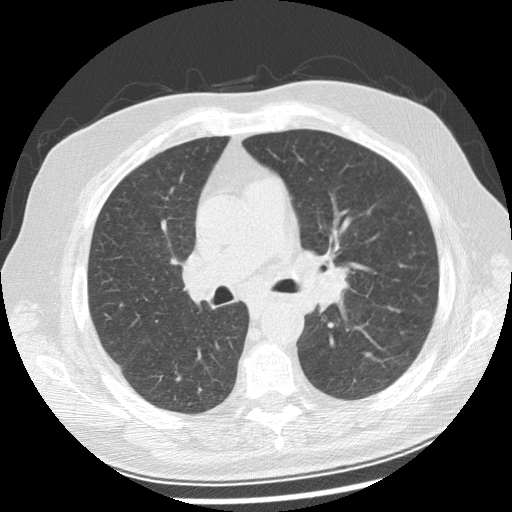
Low-dose screening chest CT, one axial slice. Slice 148 of 250 in the series (ordered by position). Lung window (W 1500 / L -600 HU). 512 × 512 image matrix, field of view 360 × 360 mm.
Structures marked on this image (manually delineated by an expert):
- lesion 1 (tumor, left main bronchus): box from (x=309, y=266) to (x=348, y=316) px